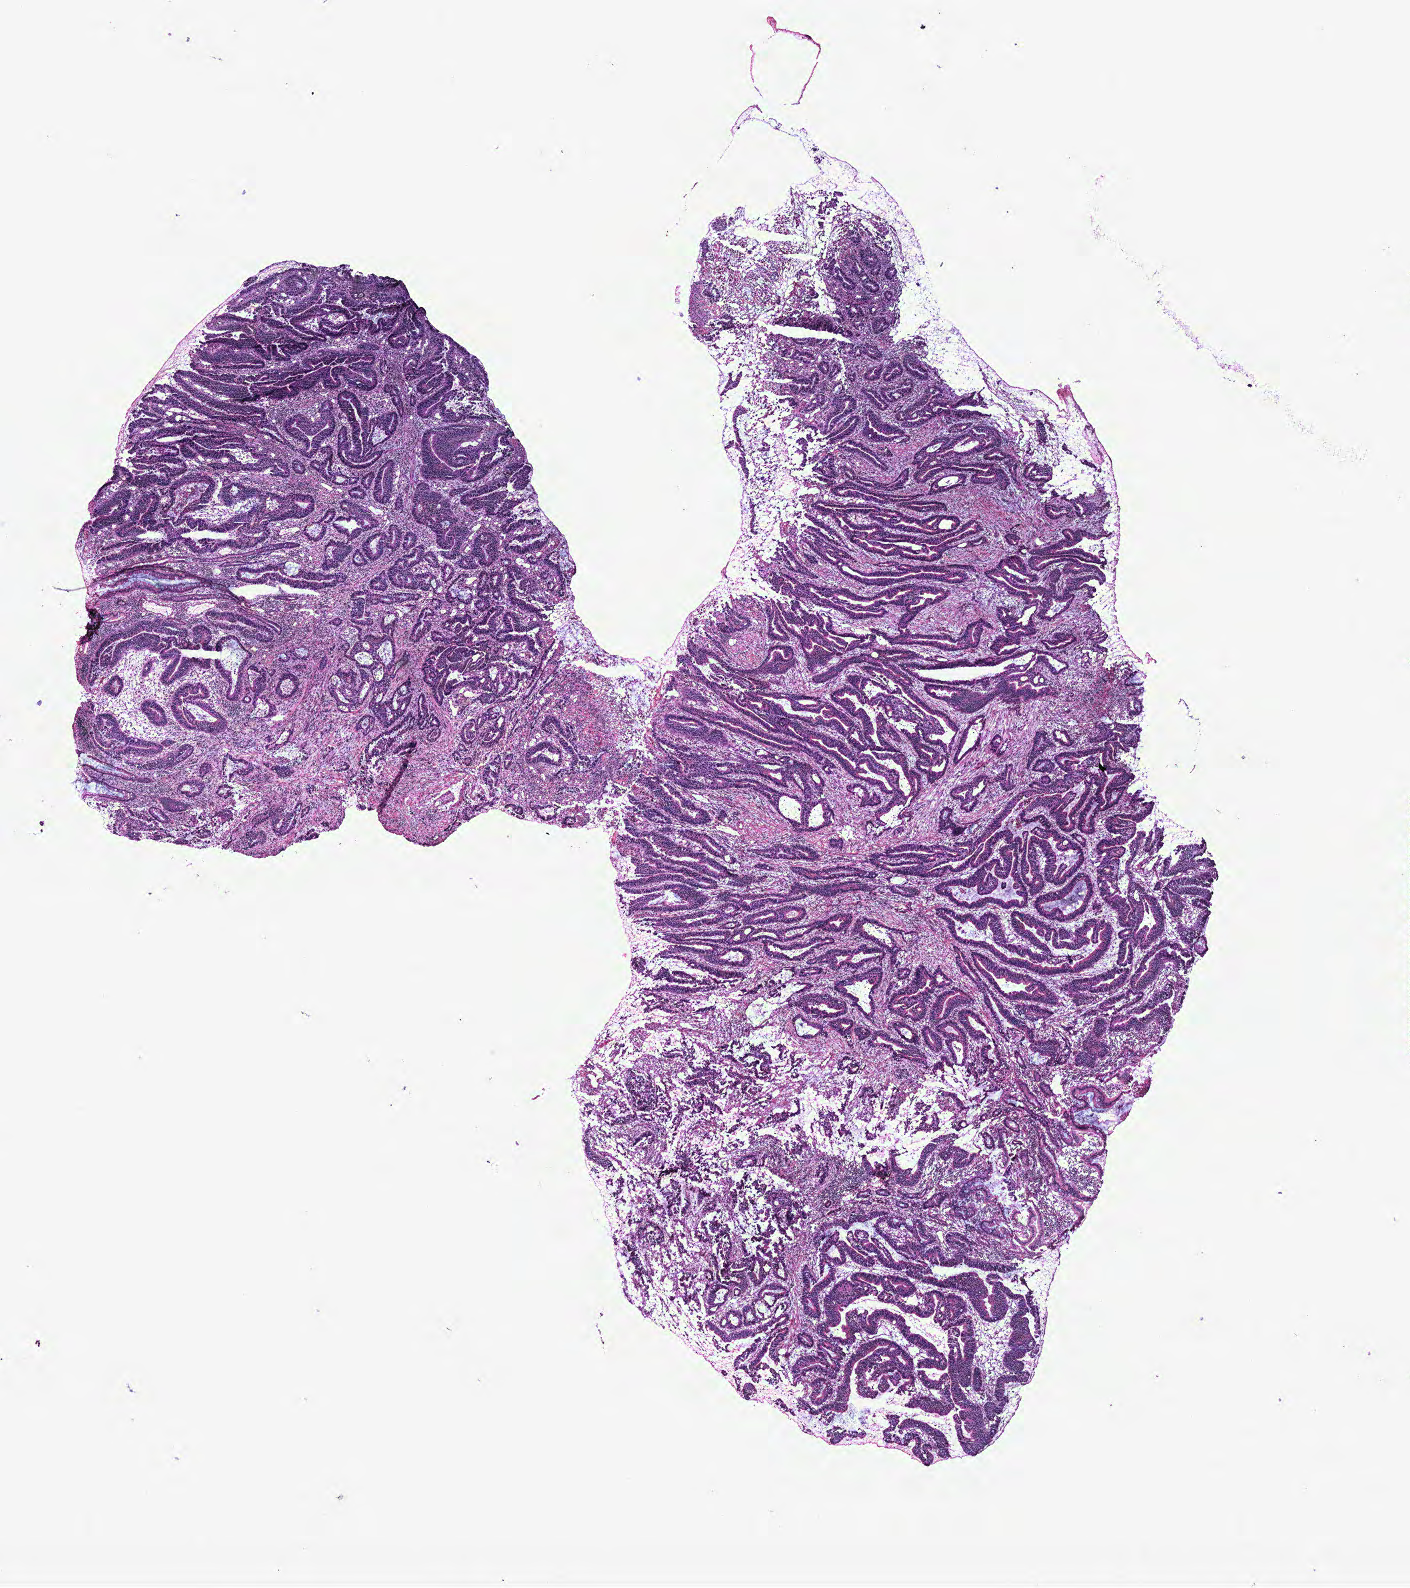
Digitized H&E-stained tissue section (whole slide) — a low-resolution overview of the entire scanned area, about 11.3 x 12.7 mm (acquisition: 40x scan). Colon, normal (non-tumour) tissue. Patient: male, age 57 years.
* this section: normal (non-tumour) tissue from the same patient
* patient diagnosis: Adenocarcinoma, NOS